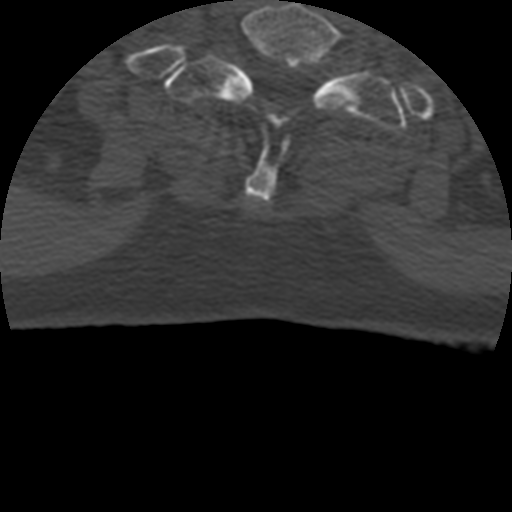
CT including the spine, one axial slice; slice 388 of 399 in the series (ordered by position); reconstruction kernel STANDARD; 120 kVp; bone window (W 1800 / L 400 HU); 512 × 512 image matrix, field of view 160 × 160 mm. Patient age 69 years. From the clinical record (not read from this slice): primary cancer: prostate.
Annotated regions visible in this slice (semi-automatic segmentation, software-assisted and operator-edited):
- T1 vertebra: bounding box (x1, y1, x2, y2) in pixels: (165, 40, 407, 130)